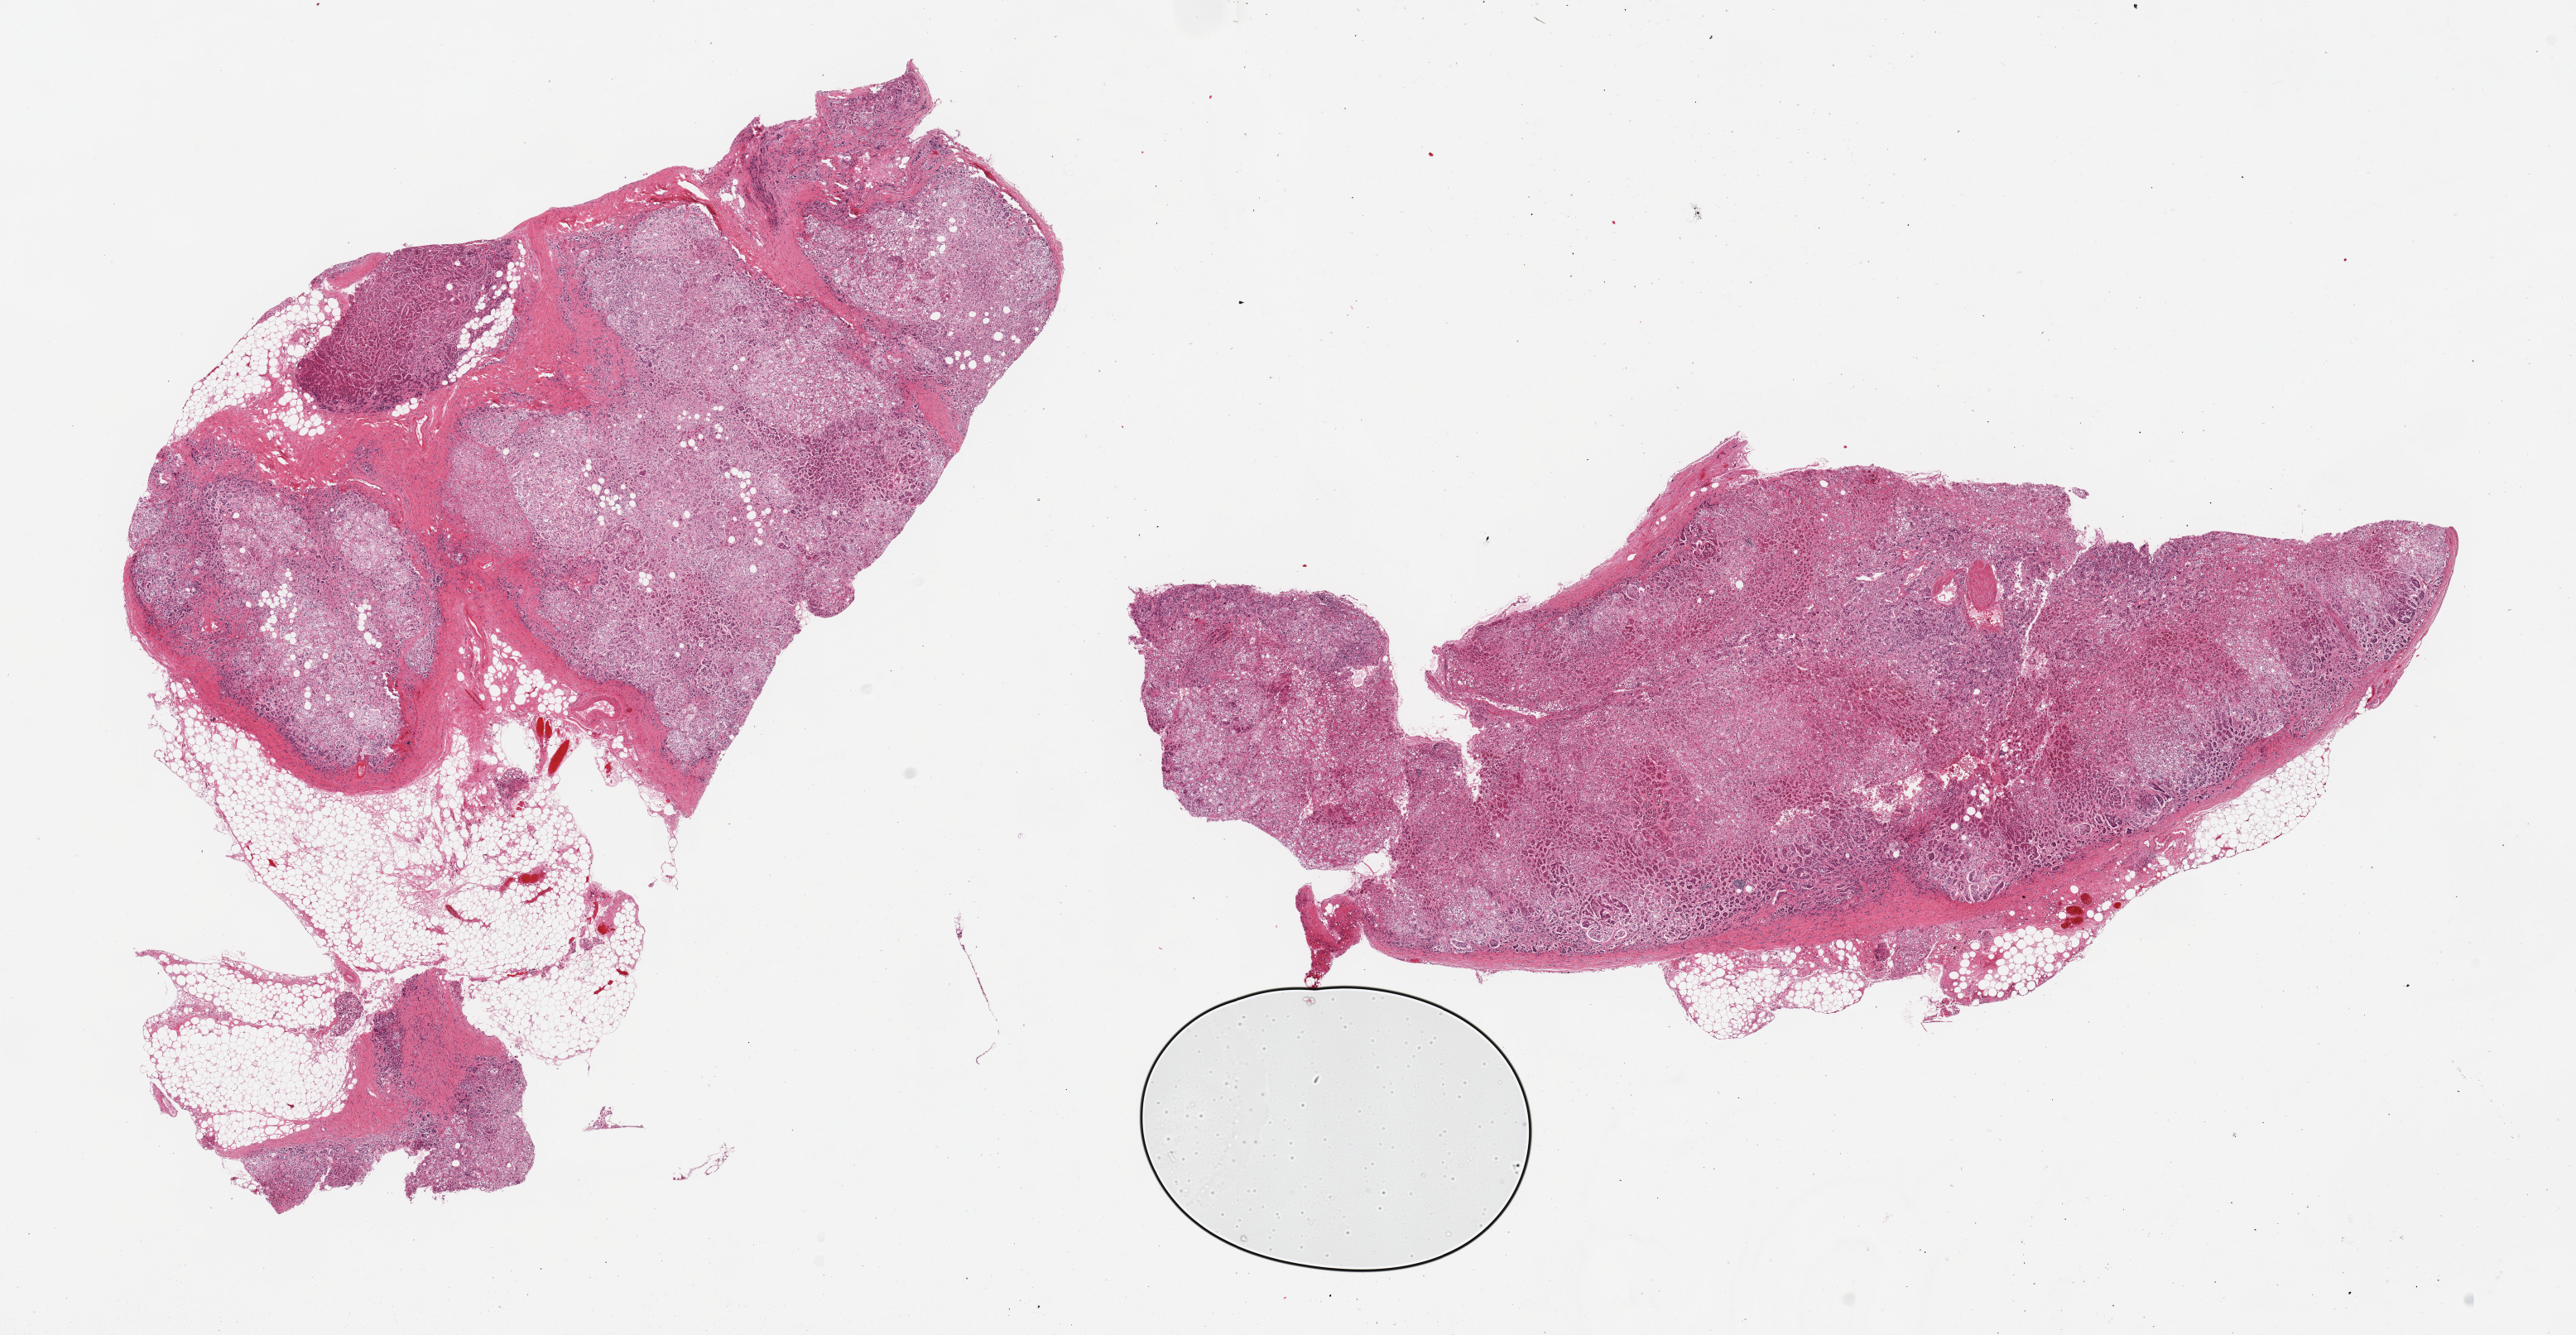
Whole-slide image, haematoxylin and eosin stain, brightfield — low-resolution overview of the scanned area, about 24.6 x 12.8 mm (slide scanned at 20x), PAXgene-fixed, paraffin-embedded tissue, target tissue: adrenal gland, donor tissue sample. Female donor.
* review note (as recorded): 2 pieces; 10% and 25% external fat